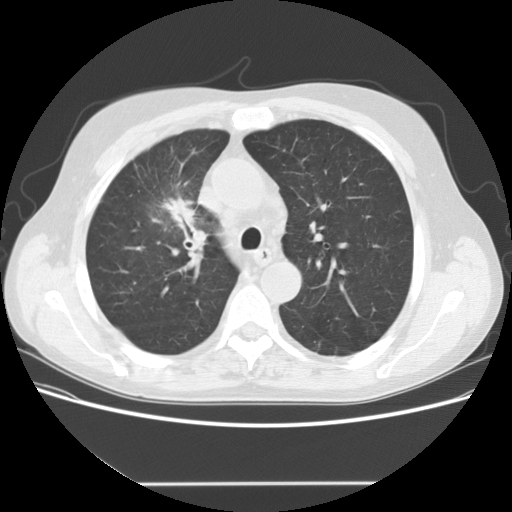
Low-dose screening chest CT, one axial slice; reconstruction kernel STANDARD; lung window (W 1500 / L -600 HU); 2.5 mm slice thickness; 512 × 512 image matrix, field of view 360 × 360 mm.
Annotated regions visible in this slice (expert manual segmentation):
- lesion 1 (tumor, upper lobe of right lung): box from (x=161, y=194) to (x=196, y=224) px